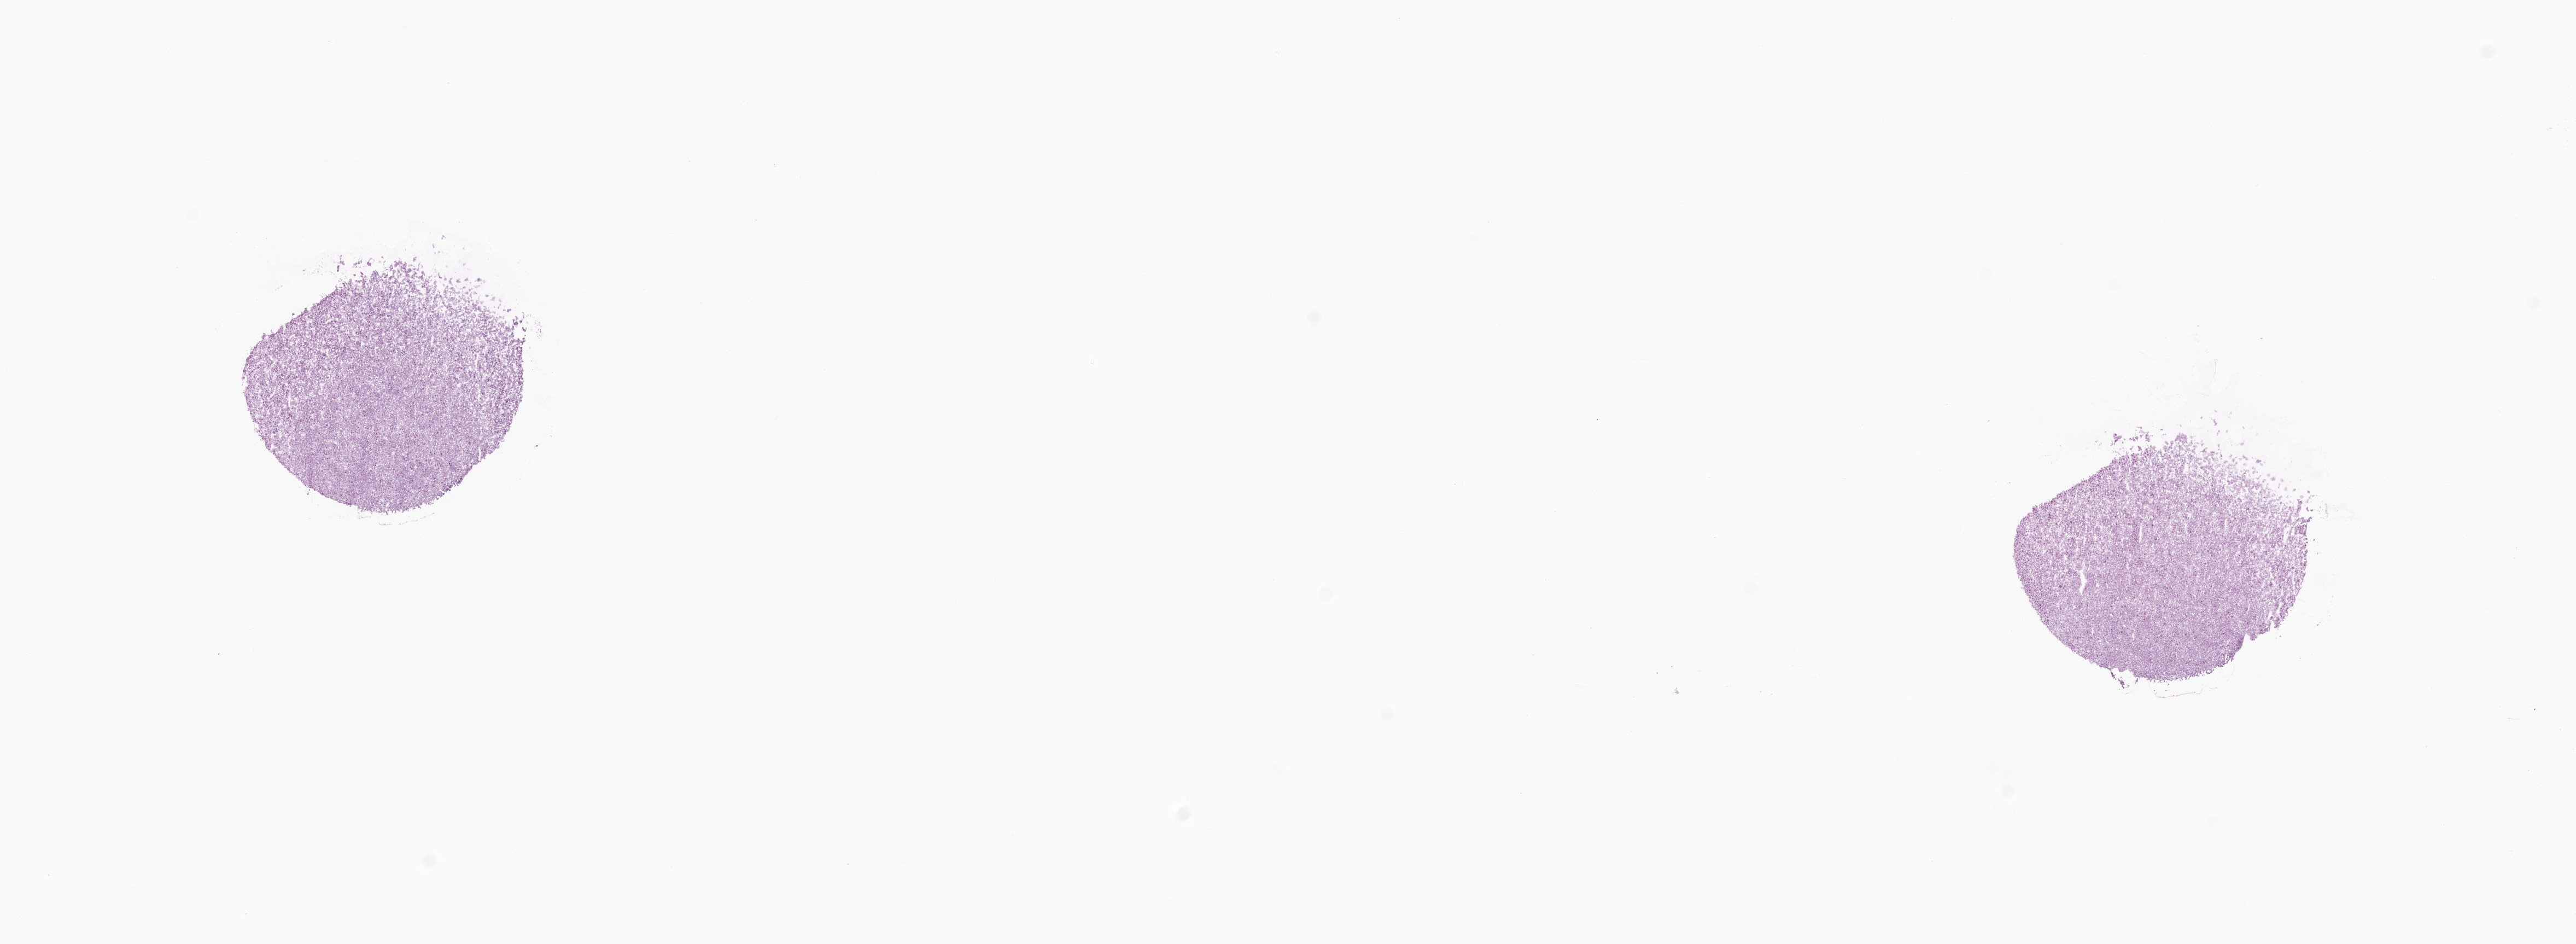
Whole-slide image, haematoxylin and eosin stain — shown as a low-resolution overview of the whole scanned area (about 19.9 x 7.3 mm); frozen section; metastatic tumor tissue, resected from peritoneum. Female patient; age at initial diagnosis 72 years. Pathologist review of this section (percent, as recorded): tumor cells 95%, tumor nuclei 95%, stromal cells 5%, necrosis 0%, normal cells 0%. Inflammatory infiltration, as recorded: lymphocyte infiltration 2%, monocyte infiltration 0%, neutrophil infiltration 1%.
Section: bottom of the tissue portion. Patient diagnosis (primary): Adenocarcinoma, metastatic, NOS.